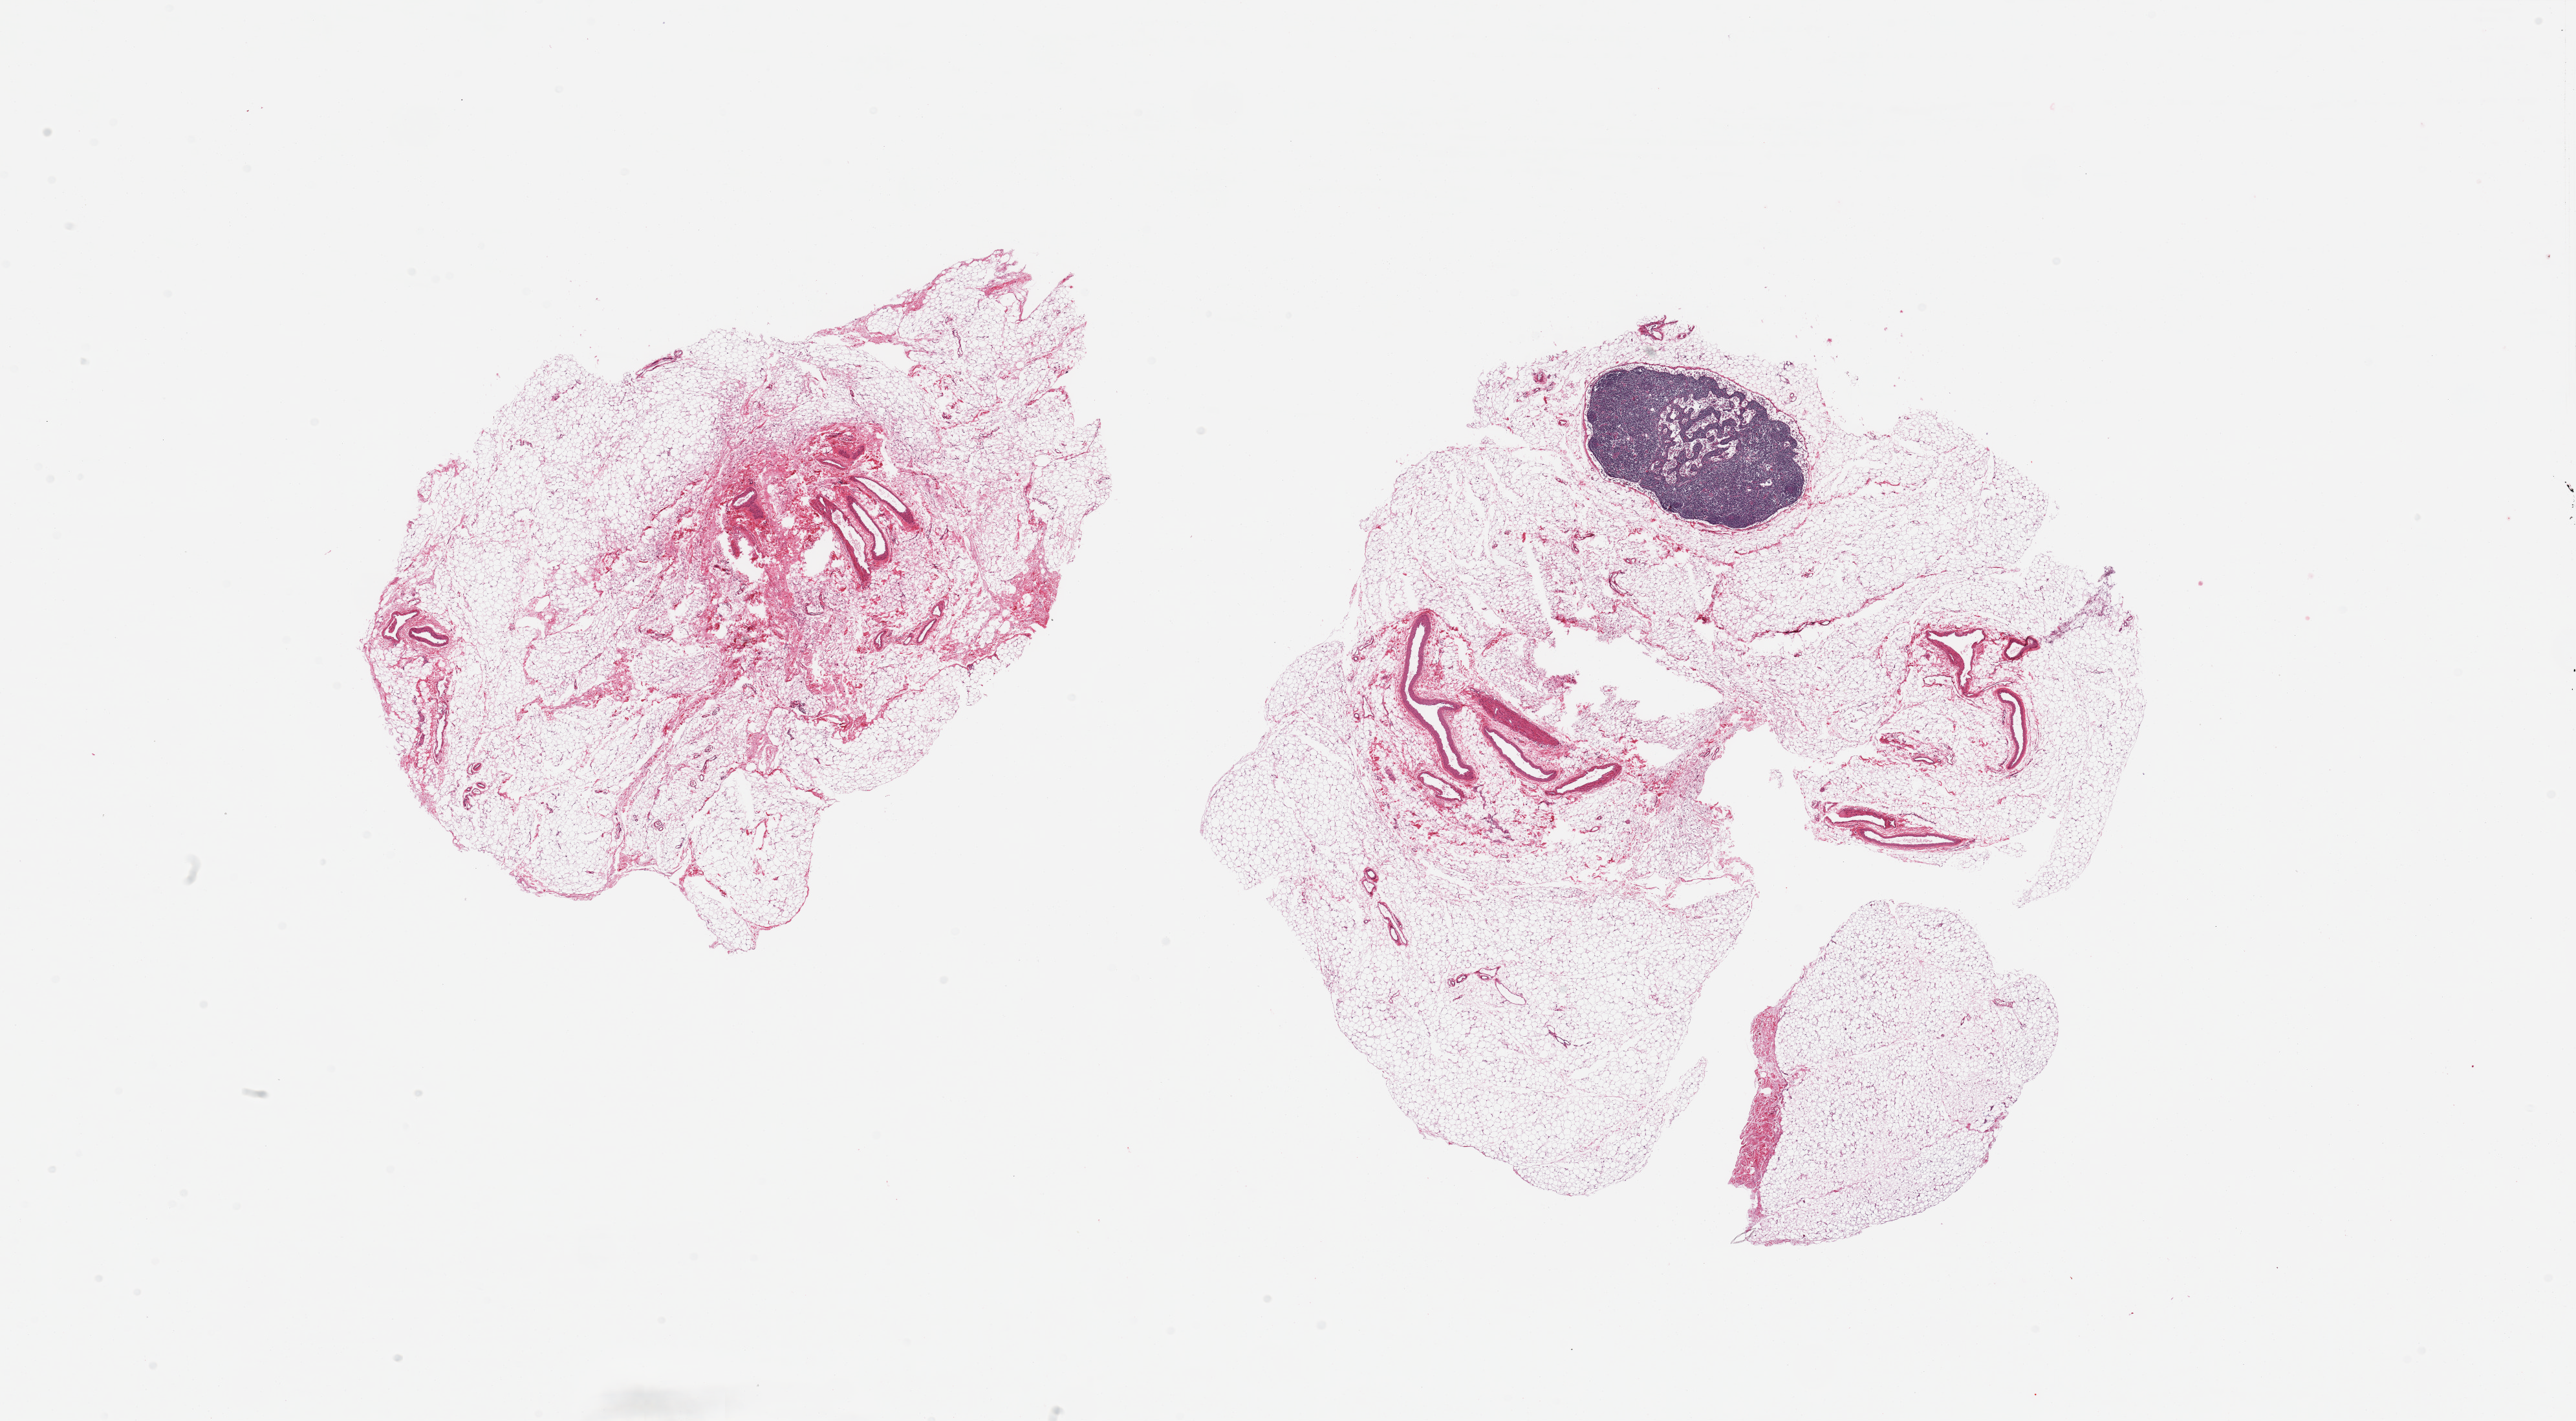
Digitized hematoxylin and eosin (H&E)-stained section, brightfield, a low-resolution overview of the entire scanned area, about 31.5 x 17.4 mm (slide scanned at 20x); PAXgene-fixed, paraffin-embedded tissue; sampled site (target tissue): omentum; donor tissue sample.
* review note (as recorded): 2 pieces; incidental ~2.5mm omental lymph node present; ~5-10% fascia, vascular elements